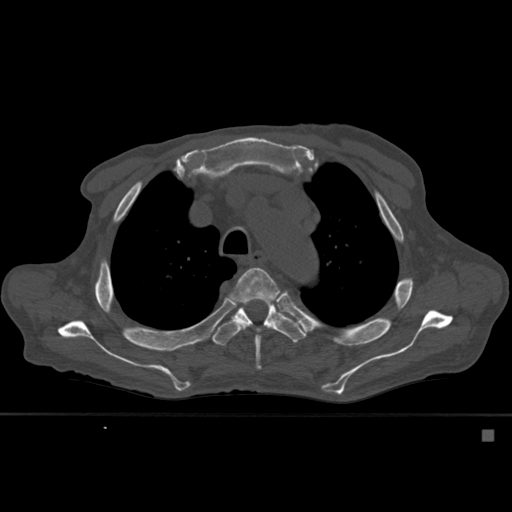
CT including the spine, one axial slice. Position 409 of 527 along the scan axis. Bone window (W 1800 / L 400 HU). 512 × 512 image matrix, field of view 373 × 373 mm. Male patient, age 78 years. From the clinical record (not read from this slice): primary cancer: prostate.
Outlined on this slice (semi-automatically segmented with operator editing):
- T4 vertebra: bounding box (x1, y1, x2, y2) in pixels: (229, 267, 281, 371)
- T5 vertebra: (212, 299, 306, 346)